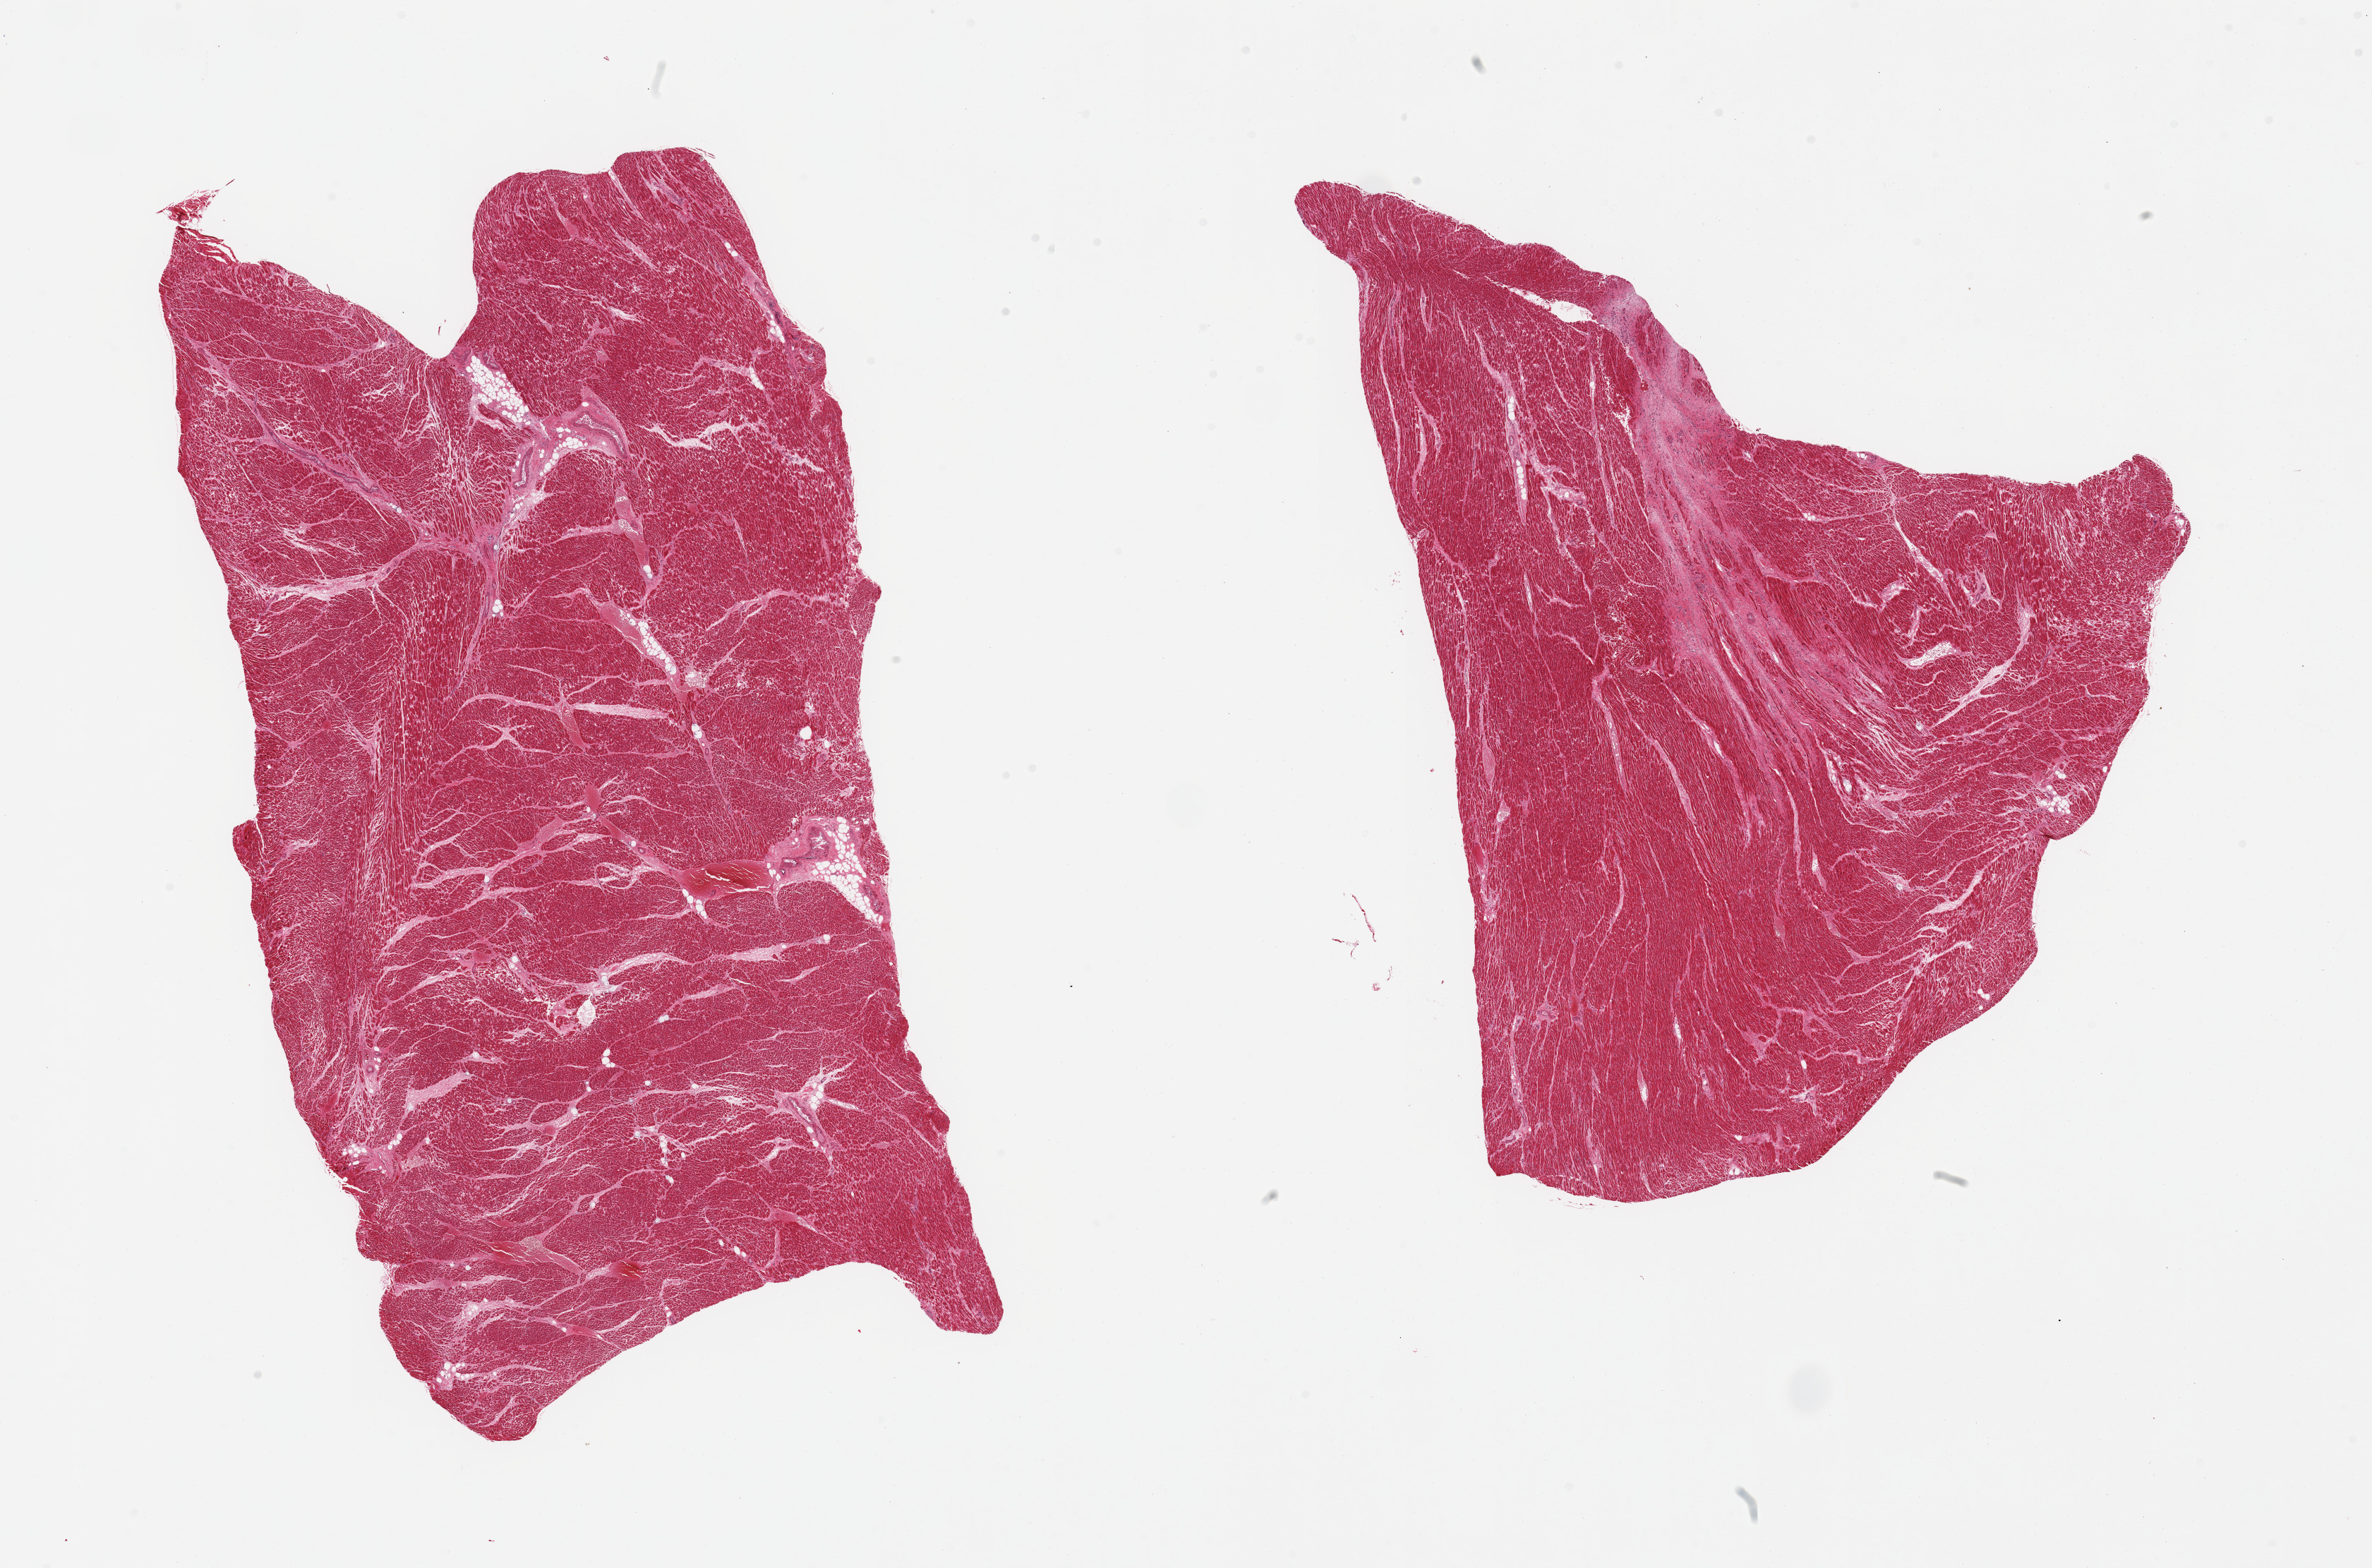
Whole-slide image, H&E stain, whole scanned area (about 26.6 x 17.6 mm, slide scanned at 20x) shown as a low-resolution overview. PAXgene-fixed paraffin-embedded (PFPE) section. Section of heart (target tissue). Donor tissue sample. Donor: male.
Review note (as recorded): 2 pieces; prominent interstitial fibrosis and focal extensive scarring.